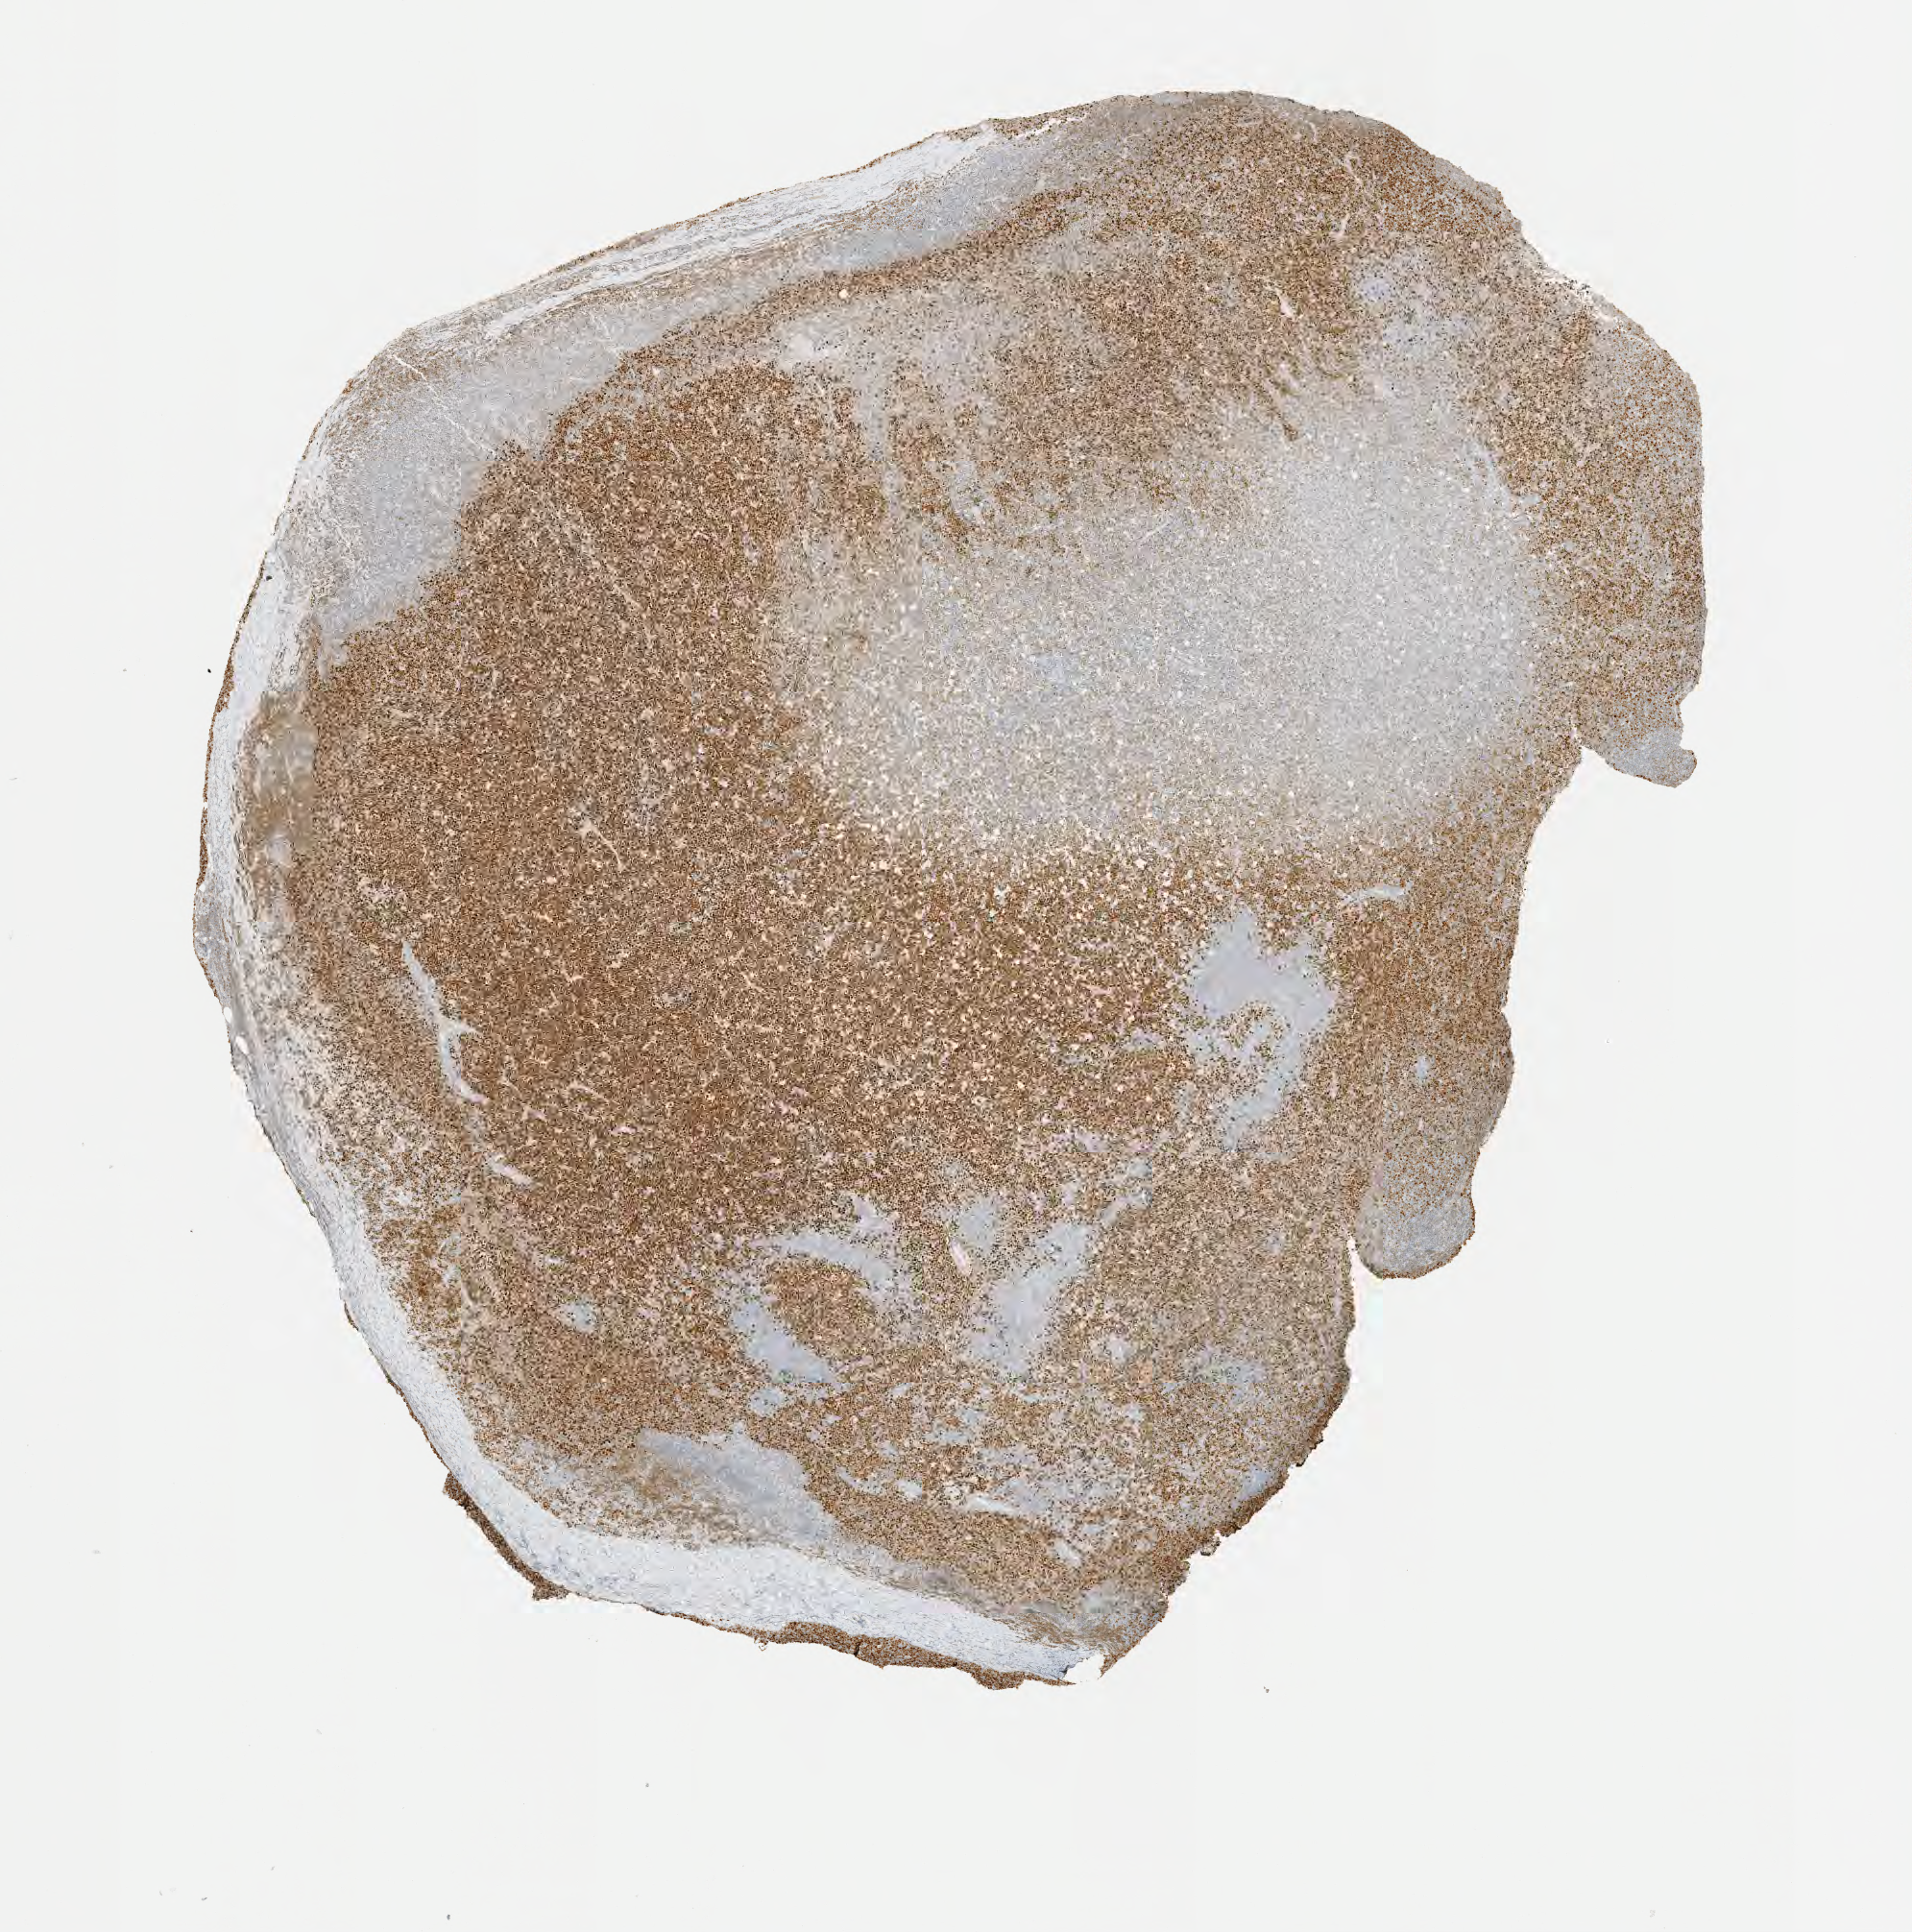
Whole-slide image, immunohistochemical stain for BCL6, a low-resolution overview of the entire scanned area, about 8.1 x 8.1 mm. Tumor tissue. Patient: male, 45 years old.
Histologic diagnosis: Burkitt lymphoma, NOS.